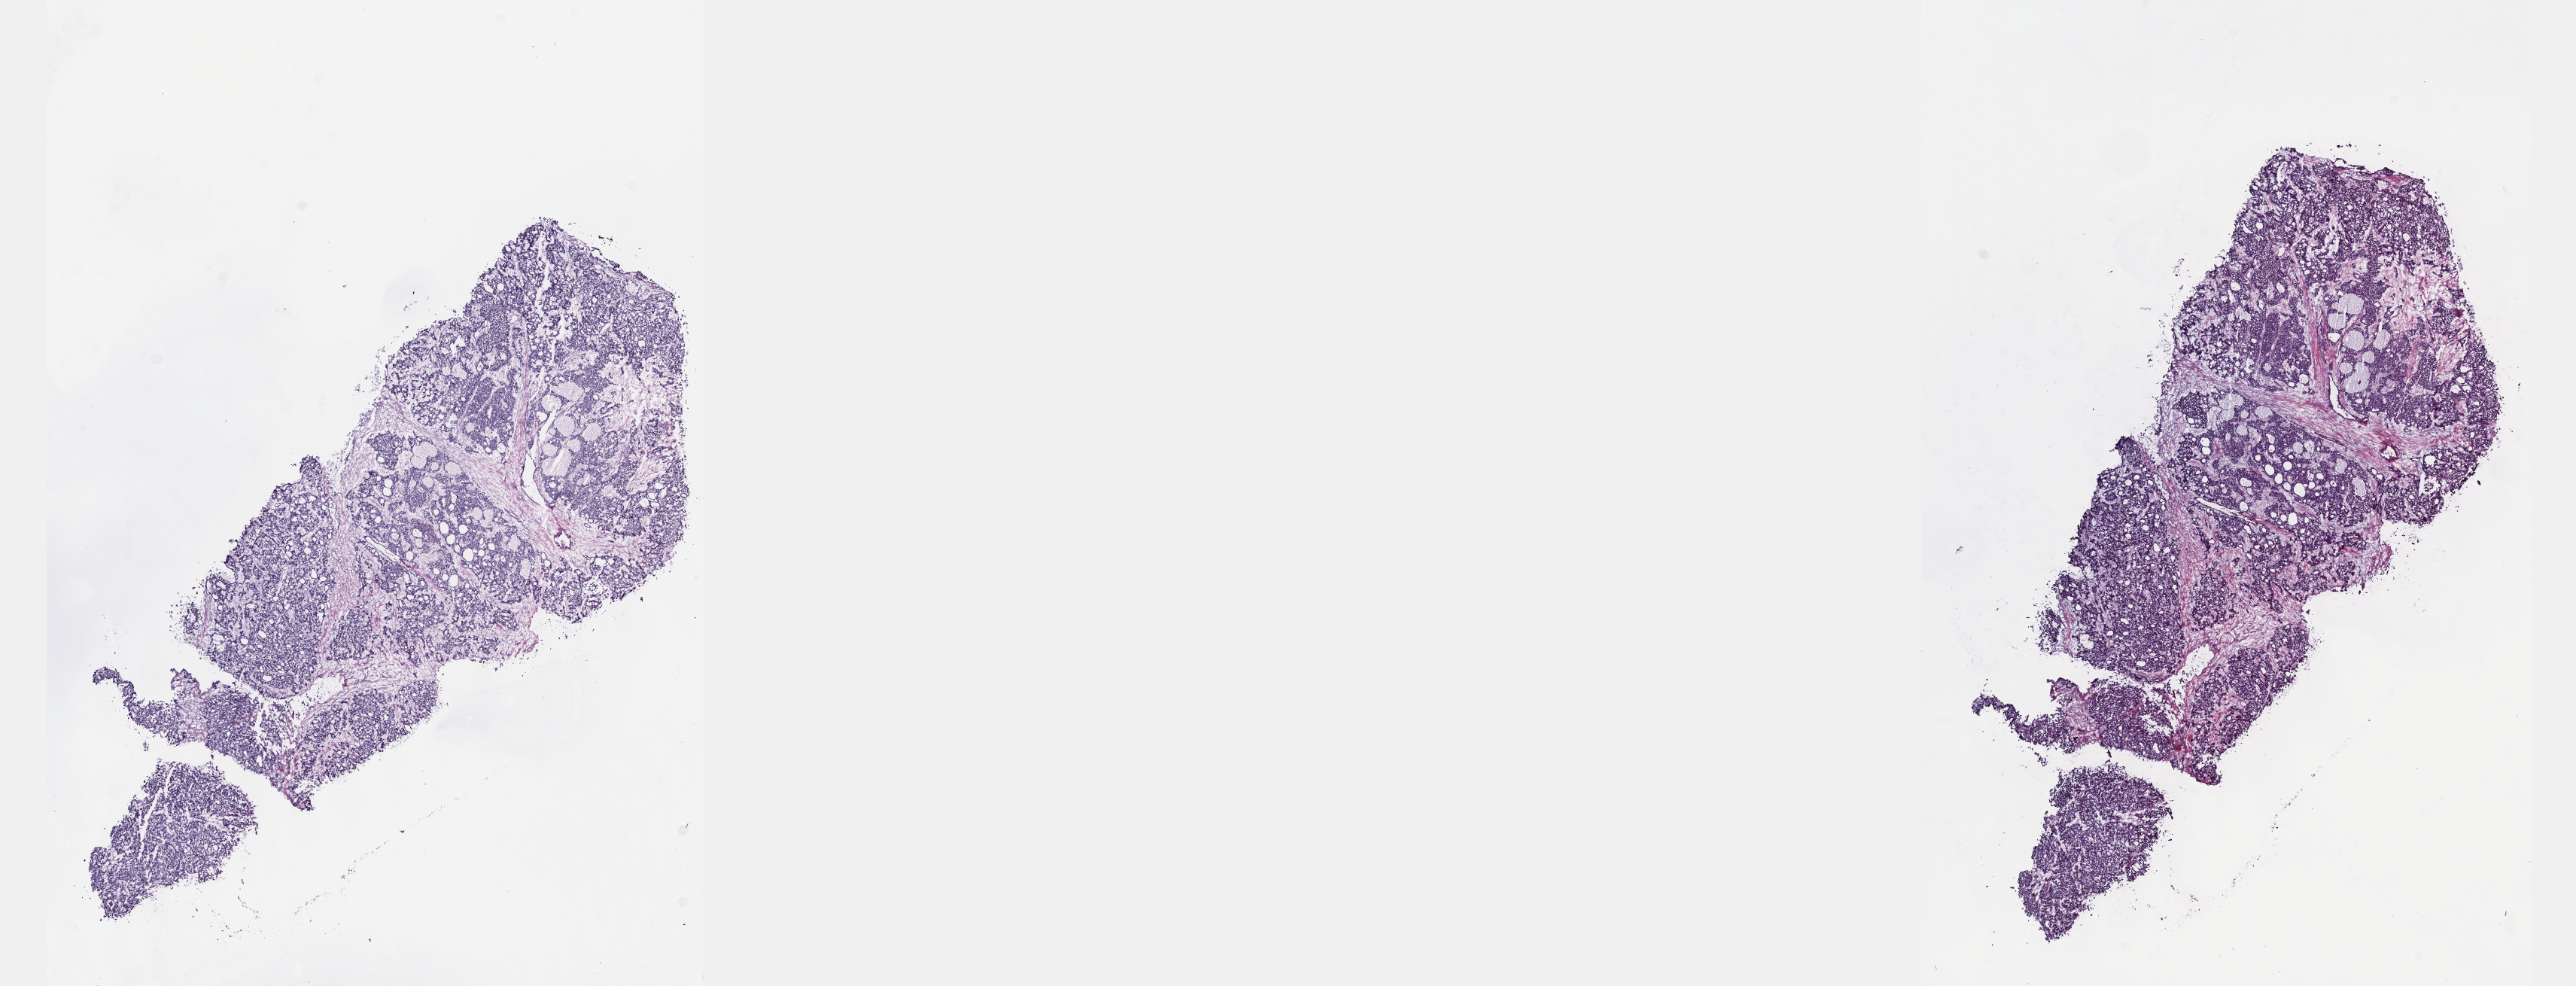
Whole-slide histology image, H&E-stained — low-resolution overview of the scanned area, about 27.7 x 10.6 mm (from a 40x scan). Frozen section from the top of the tissue portion. Sample: primary tumour, bile duct. Female patient; age at initial diagnosis 41 years. Histologic grade: G2 (moderately differentiated). Composition of this section per pathologist review: tumour cells 100%, tumour nuclei 75%, normal cells 0%, stromal cells 0%, necrosis 0%. Inflammatory infiltration, as recorded: lymphocyte infiltration 2%, monocyte infiltration 0%, neutrophil infiltration 0%.
- AJCC pathologic stage: I (7th edition)
- TNM: T1 N0 M0
- diagnosis: Cholangiocarcinoma